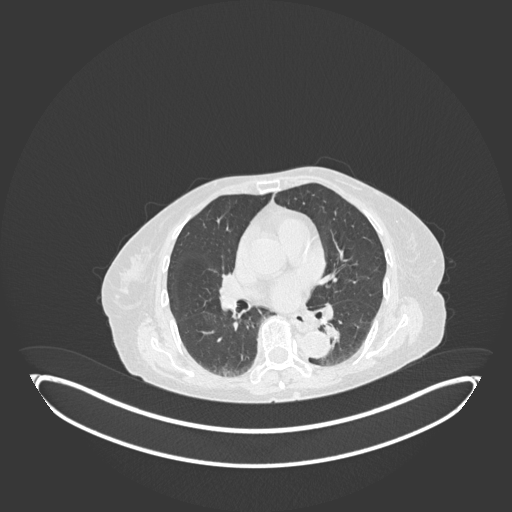
Chest CT, one axial slice; position 65 of 189 along the scan axis; 120 kVp; lung window (W 1500 / L -600 HU); 1 mm slice thickness; 512 × 512 image matrix. Patient: female, 82 years. From the clinical record (not read from this slice): clinical TNM (as recorded): T1b N0 M1.
Annotated regions visible in this slice (rectangle marked by the reading radiologist):
- lung tumour (recorded histology: adenocarcinoma): box from (x=320, y=317) to (x=346, y=351) px